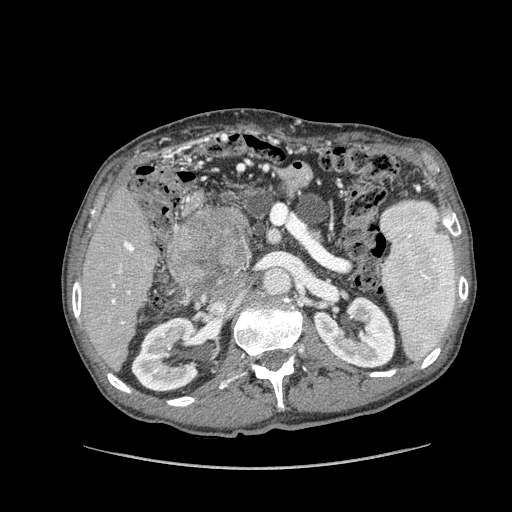
Contrast-enhanced abdominal CT (liver protocol), one axial slice. 100 kVp. Soft-tissue window (W 400 / L 40 HU). 2.5 mm slice thickness. 512 × 512 image matrix, field of view 400 × 400 mm. From the clinical record (not read from this slice): diagnosis: hepatocellular carcinoma (patient treated with transarterial chemoembolisation; whether this scan precedes or follows treatment is not stated here); TNM stage (as recorded): Stage-IIIA; Child-Pugh class: A; tumour size: 9.9 cm.
Annotated regions visible in this slice (semi-automatically segmented with operator editing):
- liver parenchyma outside the tumour (the mass and vessels are separate outlines, so this box may not span the whole liver): bounding box [x1, y1, x2, y2] px = [80, 186, 158, 368]
- mass: [170, 208, 248, 290]
- liver vessels: [111, 241, 134, 324]